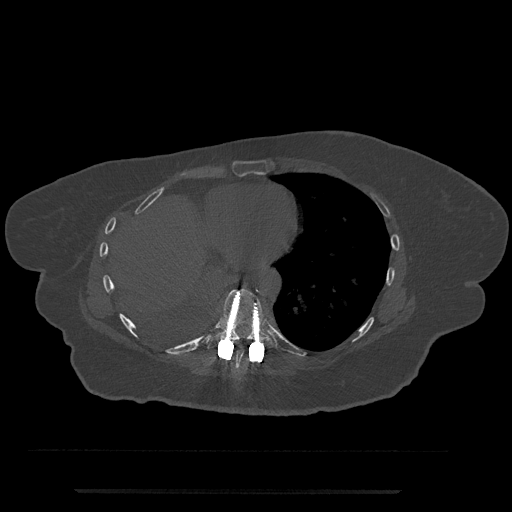
CT including the spine, one axial slice. Slice 354 of 797 in the series (ordered by position). Reconstruction kernel Br40s/3. Bone window (W 1800 / L 400 HU). 512 × 512 image matrix, field of view 440 × 440 mm. Patient: female, 51 years. From the clinical record (not read from this slice): primary cancer: neuro.
Outlined on this slice (semi-automatic segmentation, software-assisted and operator-edited):
- T8 vertebra: box from (x=231, y=346) to (x=250, y=372) px
- T9 vertebra: (x=204, y=288)–(x=275, y=348)